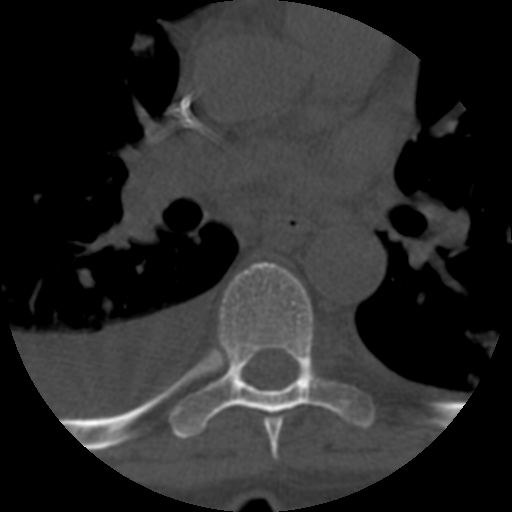
CT including the spine, one axial slice. Position 419 of 708 along the scan axis. Reconstruction kernel STANDARD. 120 kVp. One of 3 acquisitions stored at this slice position. Bone window (W 1800 / L 400 HU). 1.25 mm slice thickness. 512 × 512 image matrix, field of view 160 × 160 mm. Patient age 55 years. From the clinical record (not read from this slice): primary cancer: colon.
Structures marked on this image (semi-automatic segmentation, software-assisted and operator-edited):
- T6 vertebra: bounding box [x1, y1, x2, y2] px = [264, 418, 283, 460]
- T7 vertebra: [171, 262, 374, 440]